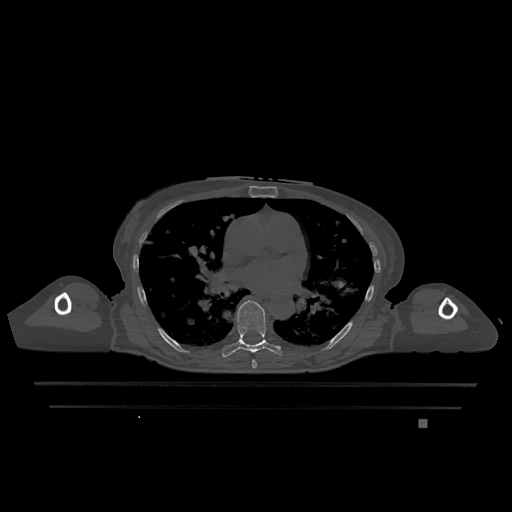
CT including the spine, one axial slice; bone window (W 1800 / L 400 HU); 512 × 512 image matrix, field of view 500 × 500 mm. Female patient, age 74 years. Case-level facts recorded for this patient, not image findings: primary cancer: lung; vertebrae with lytic lesions (as recorded): T1, T4, T5, T6, L4, L5.
Outlined on this slice (semi-automatically segmented with operator editing):
- T6 vertebra: bounding box [x1, y1, x2, y2] px = [252, 360, 257, 369]
- T7 vertebra: [222, 300, 282, 358]